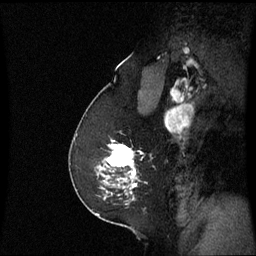
Breast MRI (dynamic contrast-enhanced), one sagittal slice; position 42 of 60 along the scan axis; dynamic contrast-enhanced series, image 2 of 3 at this slice position (ordered by acquisition); 1.5 T; TE 4.2 ms, TR 8.9 ms; 2.2 mm slice thickness; 256 × 256 image matrix. Patient: female, 58 years. From the clinical record (not read from this slice): setting: breast cancer imaged before/during neoadjuvant chemotherapy; receptor status: triple-negative.
Annotated regions visible in this slice (semi-automatic segmentation, software-assisted and operator-edited):
- analysis volume of interest (the breast-tissue region the enhancement analysis was run in; not a lesion): box from (x=96, y=140) to (x=137, y=193) px
- tumour enhancement mask (voxels above the 70 % enhancement threshold inside the analysis volume of interest): (x=106, y=140)–(x=137, y=189)